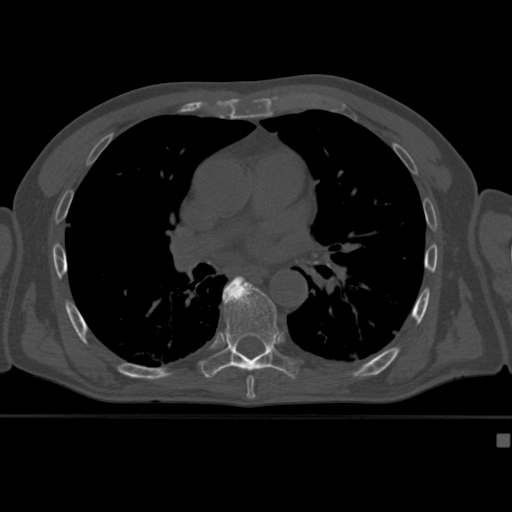
CT including the spine, one axial slice. Slice 267 of 430 in the series (ordered by position). Reconstruction kernel Br40s. Bone window (W 1800 / L 400 HU). 1.5 mm slice thickness. 512 × 512 image matrix, field of view 337 × 337 mm. Male patient, age 64 years. From the clinical record (not read from this slice): primary cancer: uterus; vertebrae with lytic lesions (as recorded): T1, T4, T5, T7, L5.
Structures marked on this image (semi-automatic segmentation, software-assisted and operator-edited):
- T7 vertebra: bounding box [x1, y1, x2, y2] px = [246, 375, 255, 382]
- T8 vertebra: [201, 276, 300, 379]